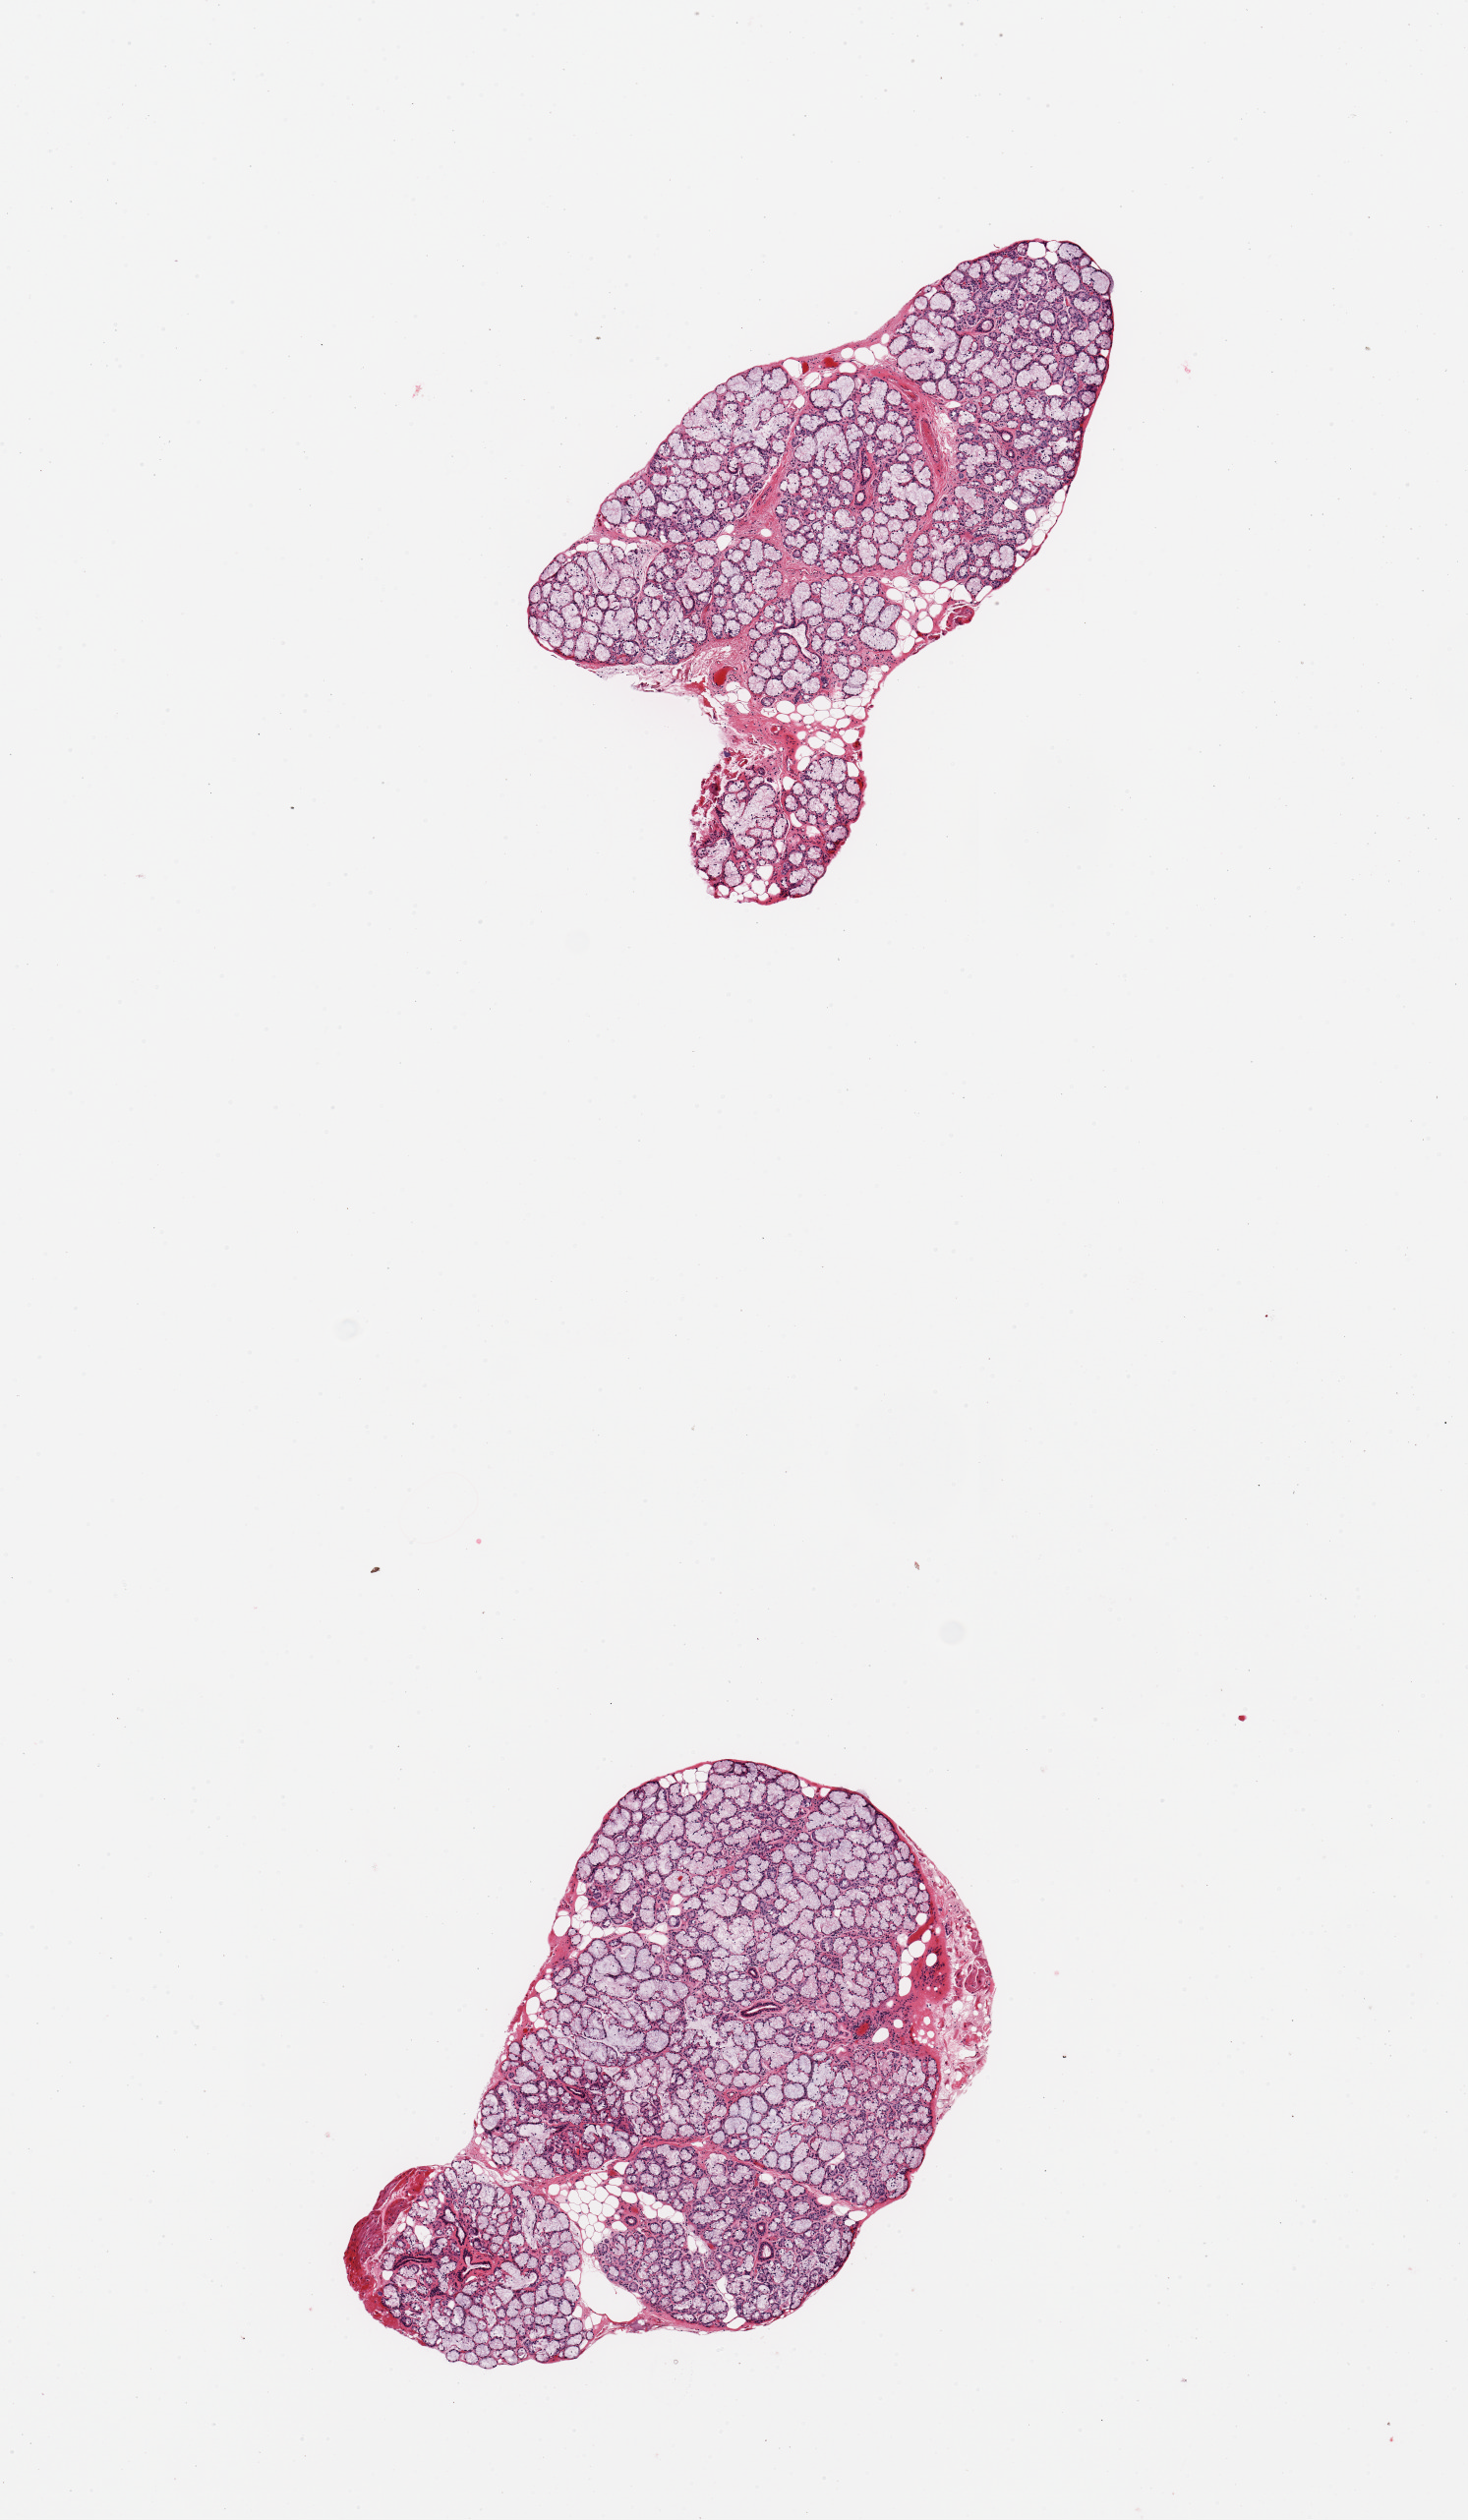
H&E whole-slide image — a low-resolution overview of the entire scanned area, about 5.9 x 10.1 mm, PAXgene-fixed, paraffin-embedded tissue, section of minor salivary gland (target tissue), donor tissue sample. Donor: male.
• reviewer comment on this tissue sample: 2 pieces; well trimmed